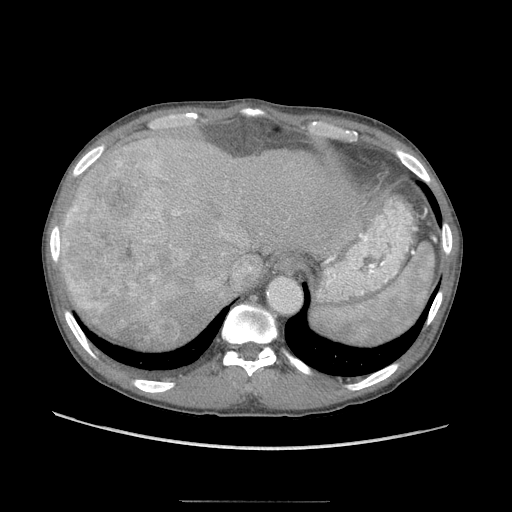
Contrast-enhanced abdominal CT (liver protocol), one axial slice; slice 77 of 103 in the series (ordered by position); reconstruction kernel STANDARD; 120 kVp; soft-tissue window (W 400 / L 40 HU); 2.5 mm slice thickness; 512 × 512 image matrix, field of view 380 × 380 mm. From the clinical record (not read from this slice): diagnosis: hepatocellular carcinoma (patient treated with transarterial chemoembolisation; whether this scan precedes or follows treatment is not stated here); TNM stage (as recorded): Stage-IIIA; Child-Pugh class: A; tumour differentiation: moderately differentiated; tumour nodularity: multinodular.
Structures marked on this image (semi-automatic segmentation, software-assisted and operator-edited):
- liver parenchyma outside the tumour (the mass and vessels are separate outlines, so this box may not span the whole liver): bounding box (x1, y1, x2, y2) in pixels: (60, 123, 401, 342)
- mass: (64, 169, 189, 337)
- liver vessels: (126, 220, 351, 309)